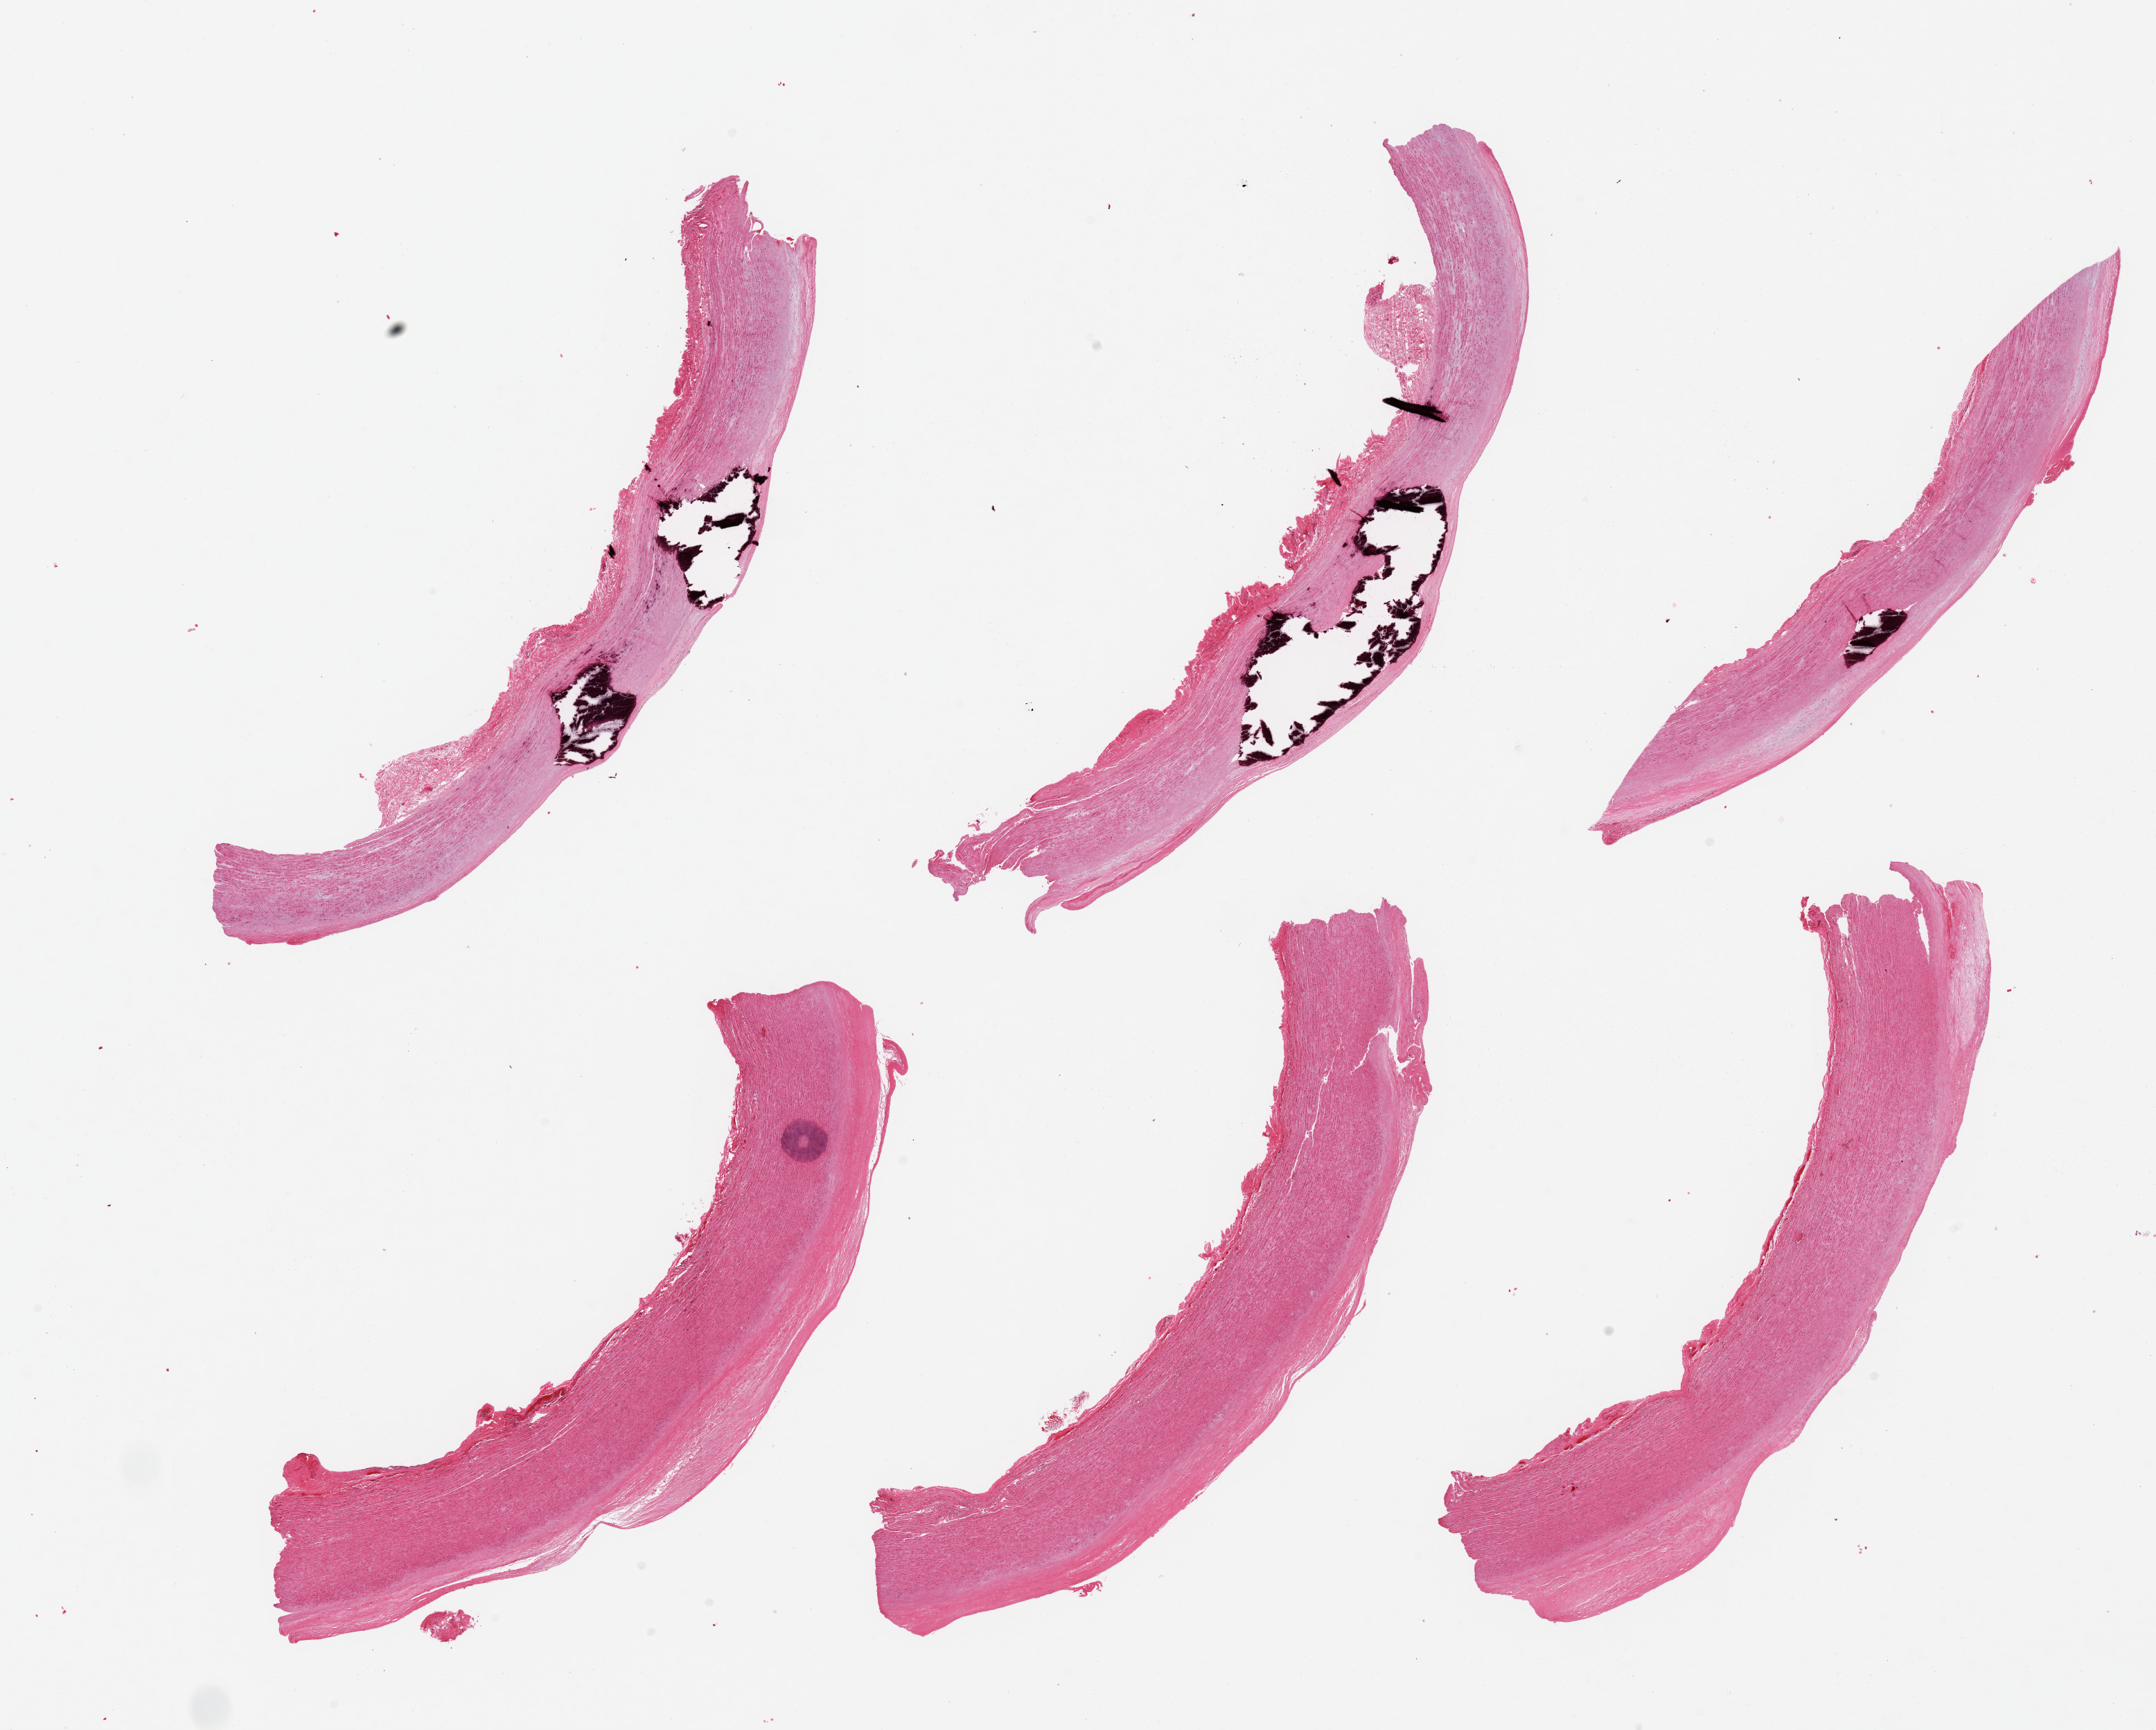
Digitized hematoxylin and eosin (H&E)-stained section, whole scanned area (about 24.6 x 19.7 mm) shown as a low-resolution overview; PAXgene-fixed paraffin-embedded (PFPE) section; target tissue: aorta; tissue donor sample. Donor: male.
Review note (as recorded): 6 pieces, calcifying atherosis up to ~0.8mm.